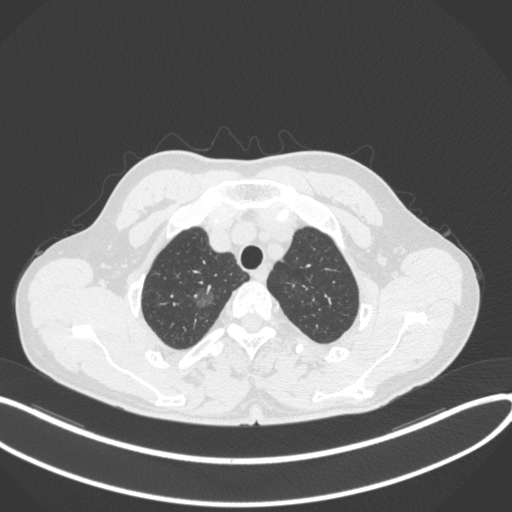
Chest CT, one axial slice. Position 324 of 407 along the scan axis. Lung window (W 1500 / L -600 HU). 1 mm slice thickness. 512 × 512 image matrix, field of view 400 × 400 mm. Patient: male, 58 years. From the clinical record (not read from this slice): clinical TNM (as recorded): T1c N0 M0; histopathological grade: G1-2.
Annotated regions visible in this slice (rectangle marked by the reading radiologist):
- lung tumour (recorded histology: adenocarcinoma): bounding box [x1, y1, x2, y2] px = [189, 278, 216, 307]